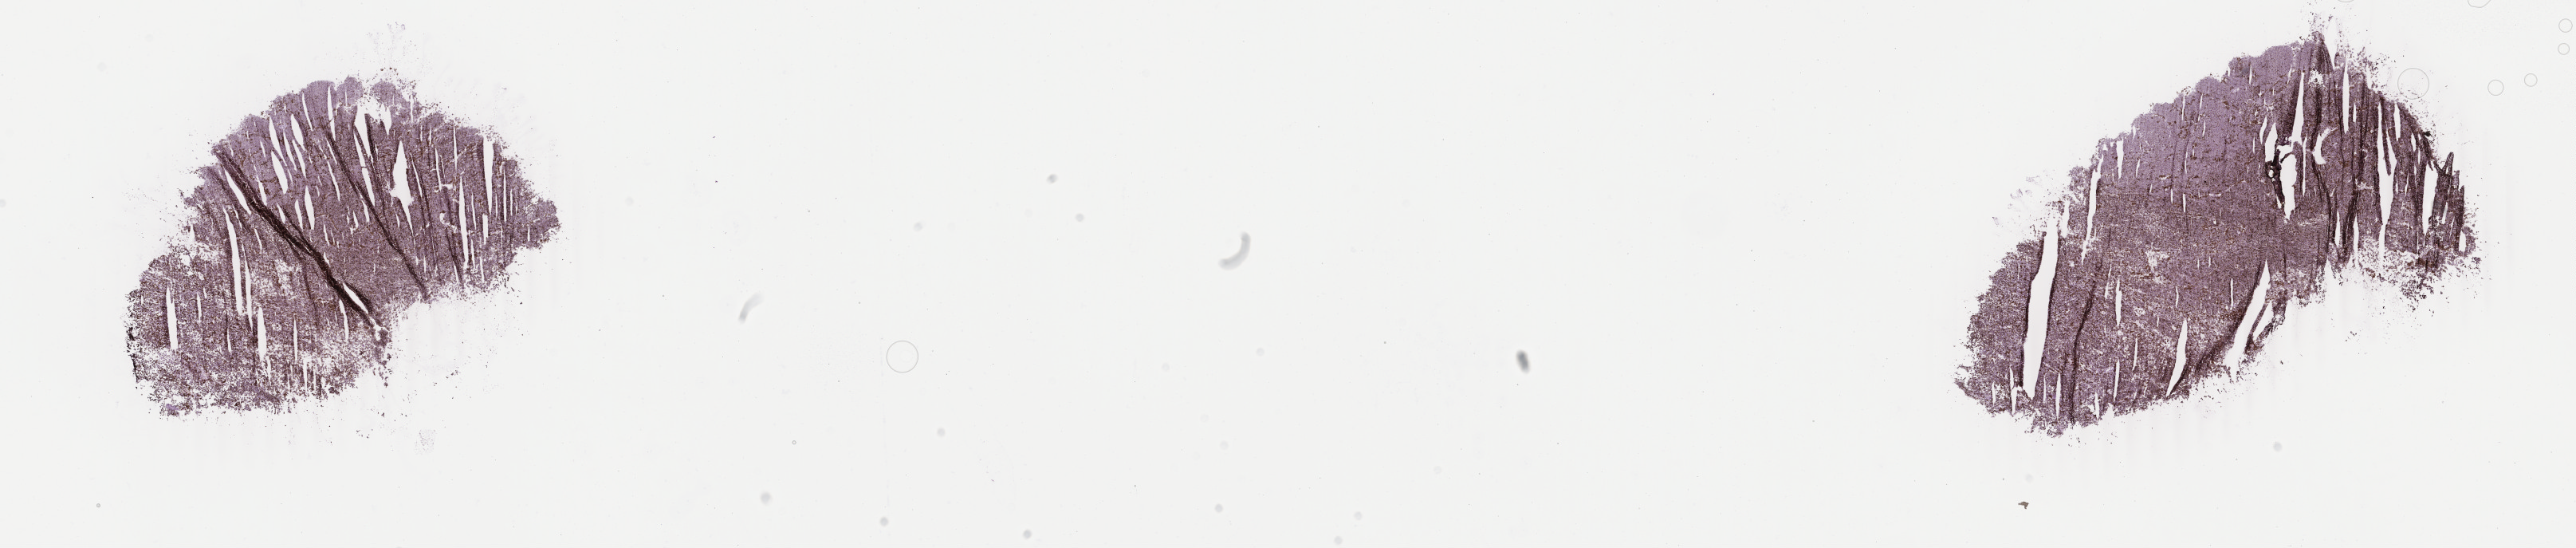
Digitized H&E-stained tissue section (whole slide), low-resolution overview of the scanned area, about 25.7 x 5.5 mm. Frozen section from the top of the tissue portion. Uvea, primary tumour sample. Male, age 59 years at initial diagnosis. Pathologist review of this section (percent, as recorded): tumour cells 100%, tumour nuclei 90%, normal cells 0%, stromal cells 0%, necrosis 0%. Inflammatory infiltration, as recorded: lymphocyte infiltration 0%, monocyte infiltration 0%, neutrophil infiltration 0%.
- diagnosis: Mixed epithelioid and spindle cell melanoma
- TNM: T4b N0 M0
- AJCC pathologic stage: IIIB (7th edition)